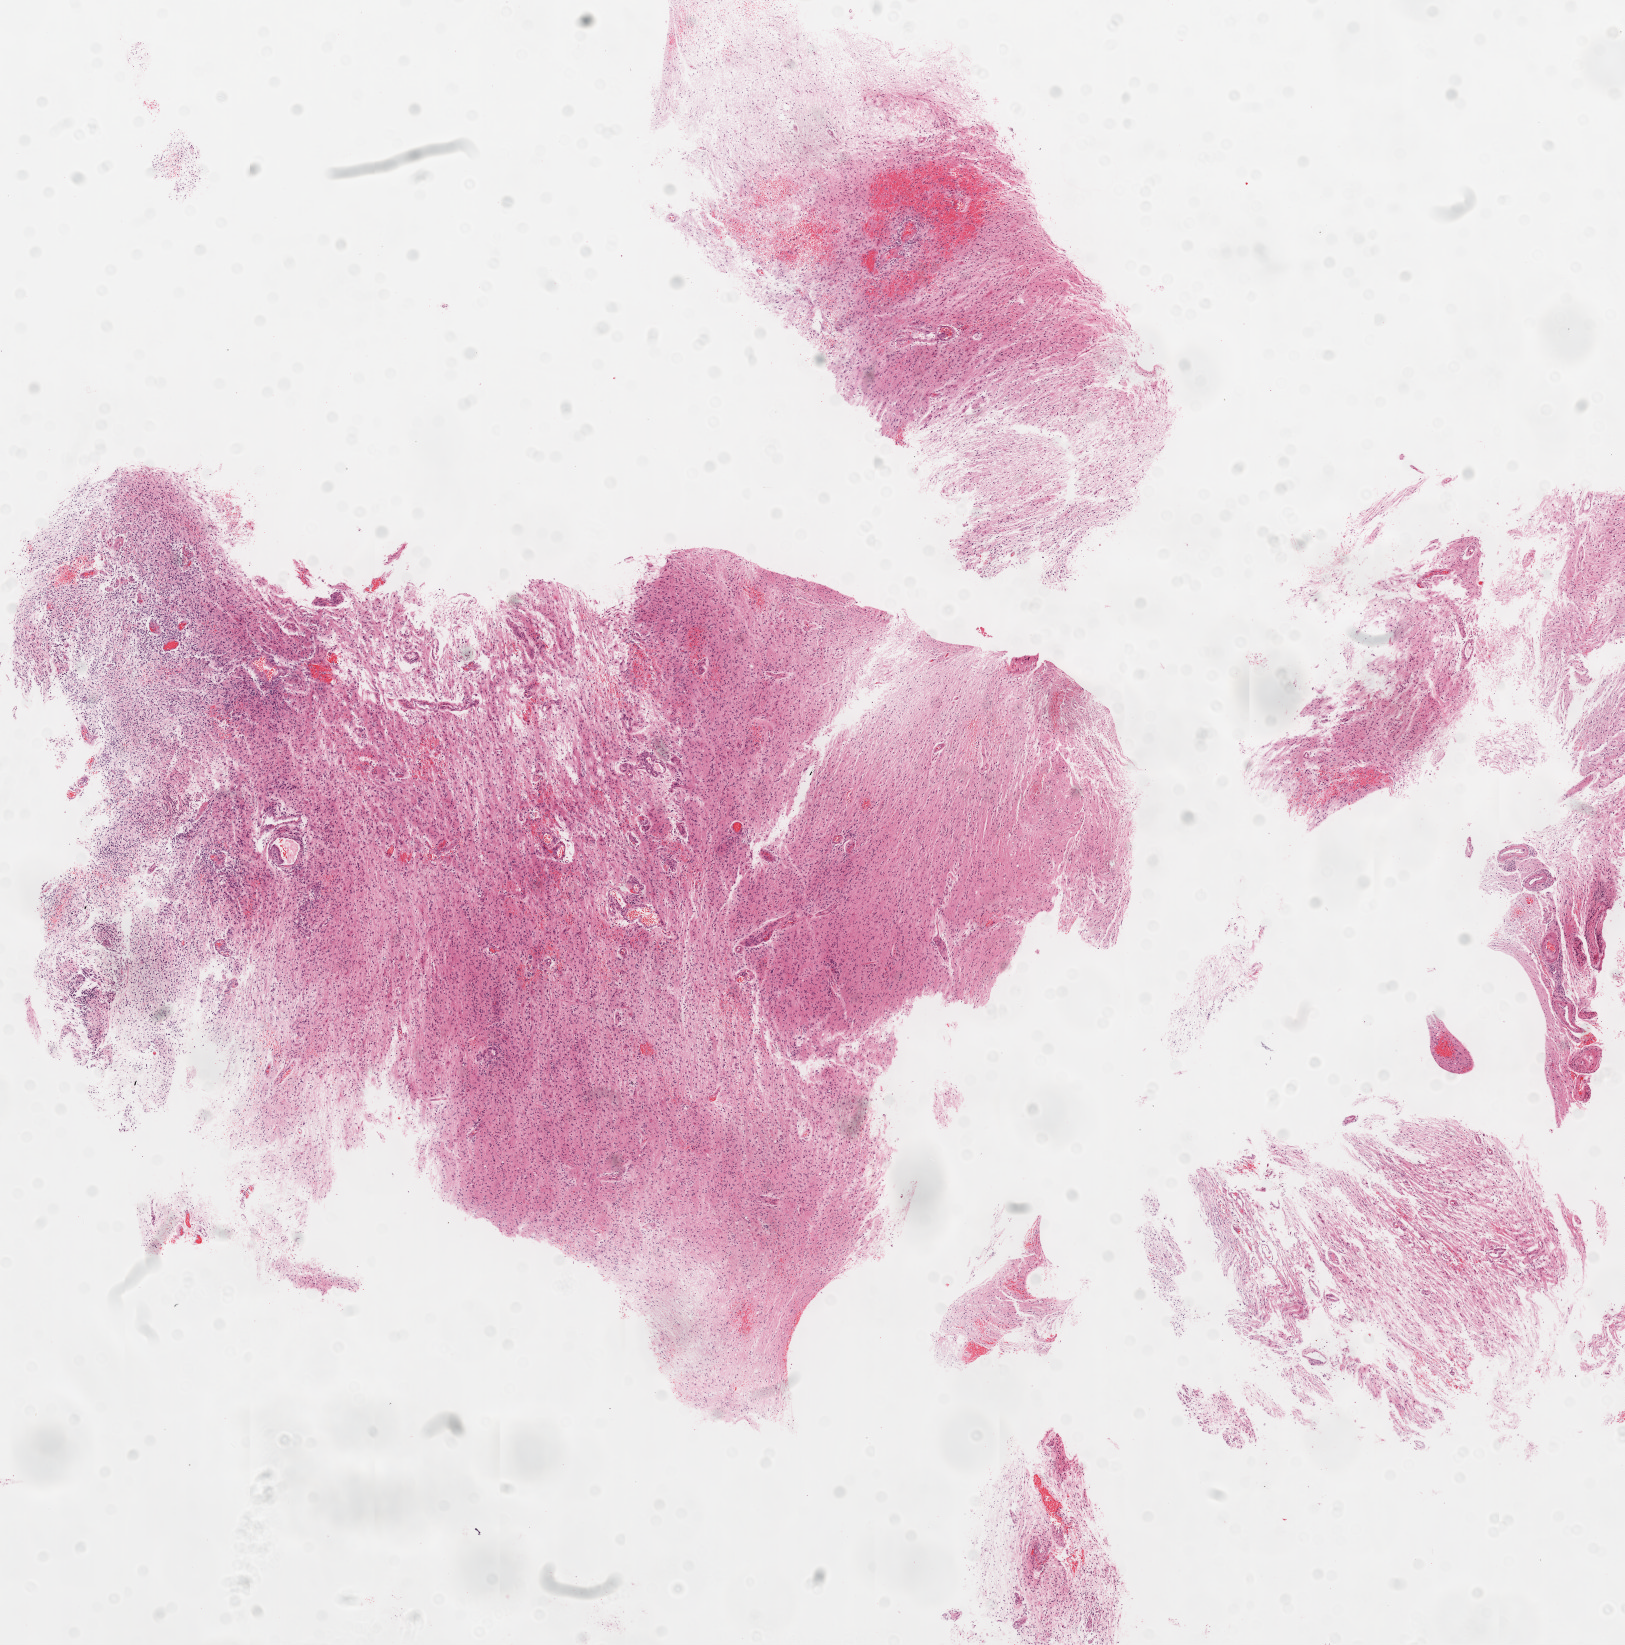
Digitized H&E-stained tissue section (whole slide), shown as a low-resolution overview of the whole scanned area (about 13.0 x 13.2 mm, slide scanned at 20x), FFPE section, primary tumour sample from the brain. Male, age 35 years at initial diagnosis.
Diagnosis: Glioblastoma.